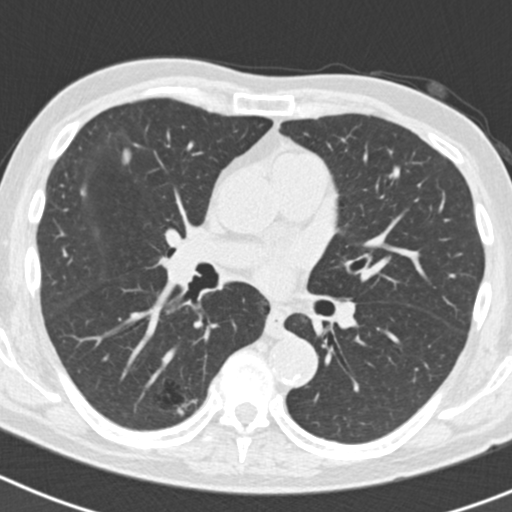
Axial slice from a low-dose chest CT screening exam; second annual screen; lung window (W 1500 / L -600 HU); standard (soft-tissue) reconstruction kernel (B30f); slice 82 of 186 in the series; 512 × 512 image matrix. Male participant, aged 70 years at enrolment.
Expert-annotated lung lesion, bounding box <130,370,200,432> (left, top, right, bottom; pixels). The screening reader recorded 5 non-calcified nodules or masses ≥4 mm on this exam (right lower lobe, right lower lobe, right upper lobe, right upper lobe, left upper lobe); which of them this box marks is not recorded. Official screen result: positive, other. Participant outcome: lung cancer diagnosed 622 days after this screen — bronchiolo-alveolar adenocarcinoma, NOS, right lower lobe, poorly differentiated (G3), stage IB (AJCC 6th edition), 30 mm at pathology.